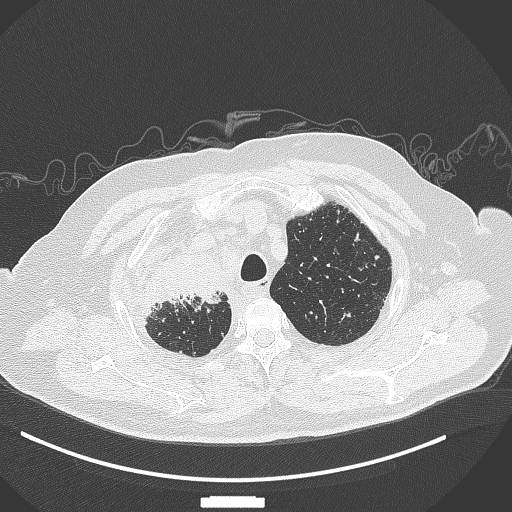
Chest CT, one axial slice; slice 306 of 384 in the series (ordered by position); lung window (W 1500 / L -600 HU); 512 × 512 image matrix. Male patient, age 69 years. Case-level facts recorded for this patient, not image findings: clinical TNM (as recorded): T4 N3 M1.
Structures marked on this image (bounding box drawn by a radiologist):
- lung tumour (recorded histology: adenocarcinoma): bounding box <137,246,227,316> (left, top, right, bottom; pixels)